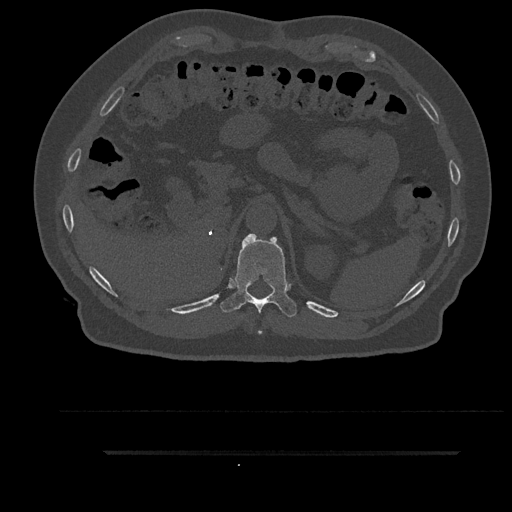
CT including the spine, one axial slice. Position 307 of 797 along the scan axis. Reconstruction kernel Br40s/3. 120 kVp. Bone window (W 1800 / L 400 HU). 0.5 mm slice thickness. 512 × 512 image matrix, field of view 432 × 432 mm. Patient: male, 63 years. From the clinical record (not read from this slice): primary cancer: renal; vertebrae with lytic lesions (as recorded): T8.
Structures marked on this image (semi-automatically segmented with operator editing):
- T11 vertebra: bounding box <220,234,297,334> (left, top, right, bottom; pixels)